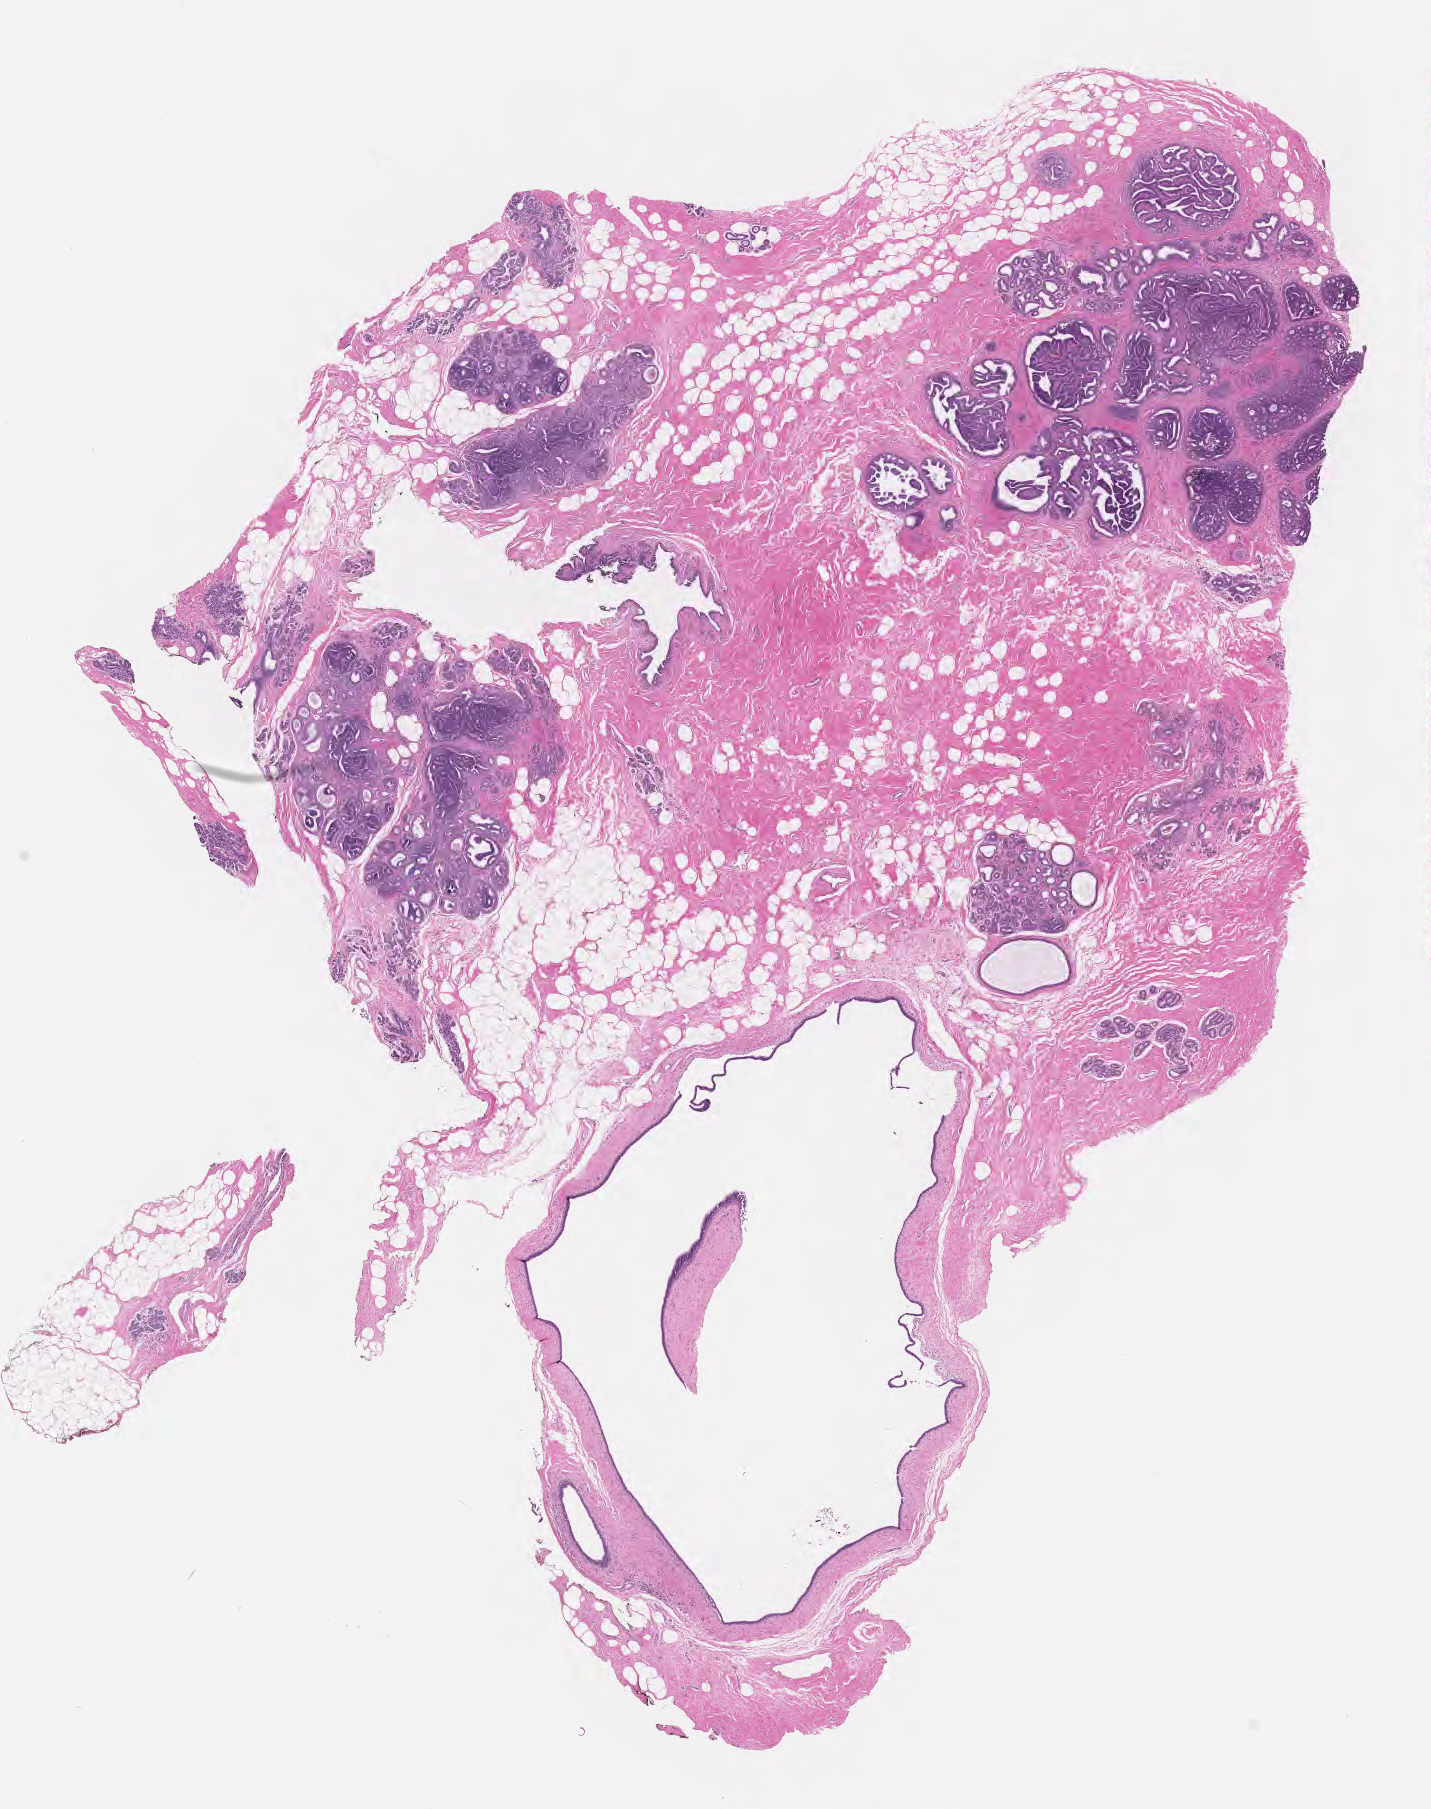
Haematoxylin and eosin whole-slide image — a low-resolution overview of the entire scanned area, about 11.6 x 14.6 mm, formalin-fixed paraffin-embedded section, premalignant lesion from a patient with intraductal carcinoma, noninfiltrating, NOS, anatomic site: breast. Female, age 49 years at initial diagnosis. Slide review estimates, as recorded: tumor cells 60%, tumor nuclei 60%, stromal cells 10%, necrosis 0%, normal cells 30%. Infiltration values recorded for this section: lymphocyte infiltration 2%, monocyte infiltration 1%, neutrophil infiltration 3%.
• this section: sample classed premalignant; the patient's recorded diagnosis is given above